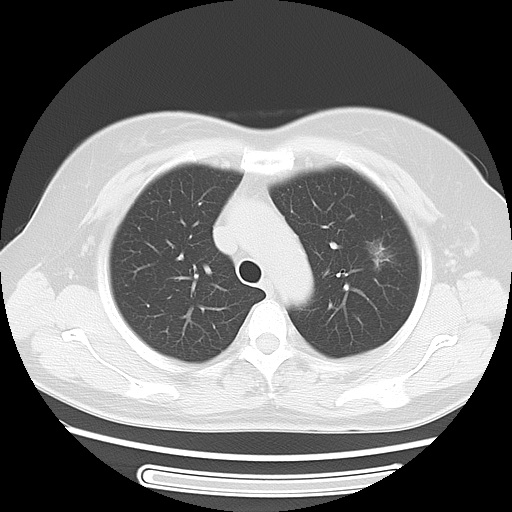
Chest CT, one axial slice. Slice 37 of 52 in the series (ordered by position). Lung window (W 1500 / L -600 HU). 5 mm slice thickness. 512 × 512 image matrix, field of view 350 × 350 mm. Female patient, age 54 years. Case-level facts recorded for this patient, not image findings: clinical TNM (as recorded): T1c N0 M0; histopathological grade: G1.
Annotated regions visible in this slice (bounding box drawn by a radiologist):
- lung tumour (recorded histology: adenocarcinoma): box from (x=360, y=233) to (x=395, y=282) px